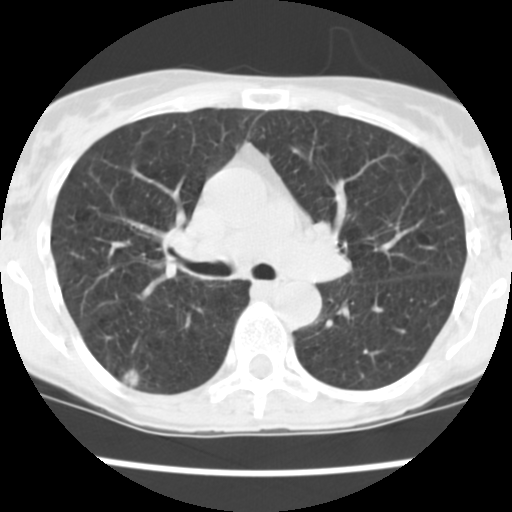
Low-dose screening chest CT, one axial slice. Position 152 of 252 along the scan axis. Reconstruction kernel STANDARD. Lung window (W 1500 / L -600 HU). 2.5 mm slice thickness. 512 × 512 image matrix, field of view 276 × 276 mm.
Annotated regions visible in this slice (outlined manually by an expert reader):
- lesion 1 (tumor, upper lobe of right lung): box from (x=123, y=370) to (x=139, y=386) px